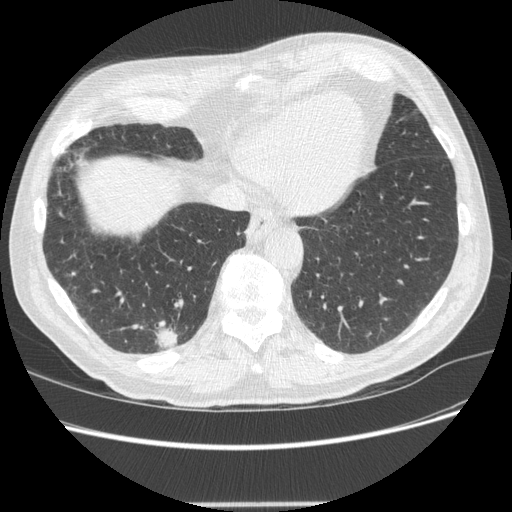
Low-dose screening chest CT, one axial slice. Slice 60 of 245 in the series (ordered by position). Reconstruction kernel STANDARD. 120 kVp. Lung window (W 1500 / L -600 HU). 1.25 mm slice thickness. 512 × 512 image matrix, field of view 372 × 372 mm.
Annotated regions visible in this slice (expert manual segmentation):
- lesion 1 (tumor, lower lobe of right lung): bounding box (x1, y1, x2, y2) in pixels: (157, 327, 178, 349)